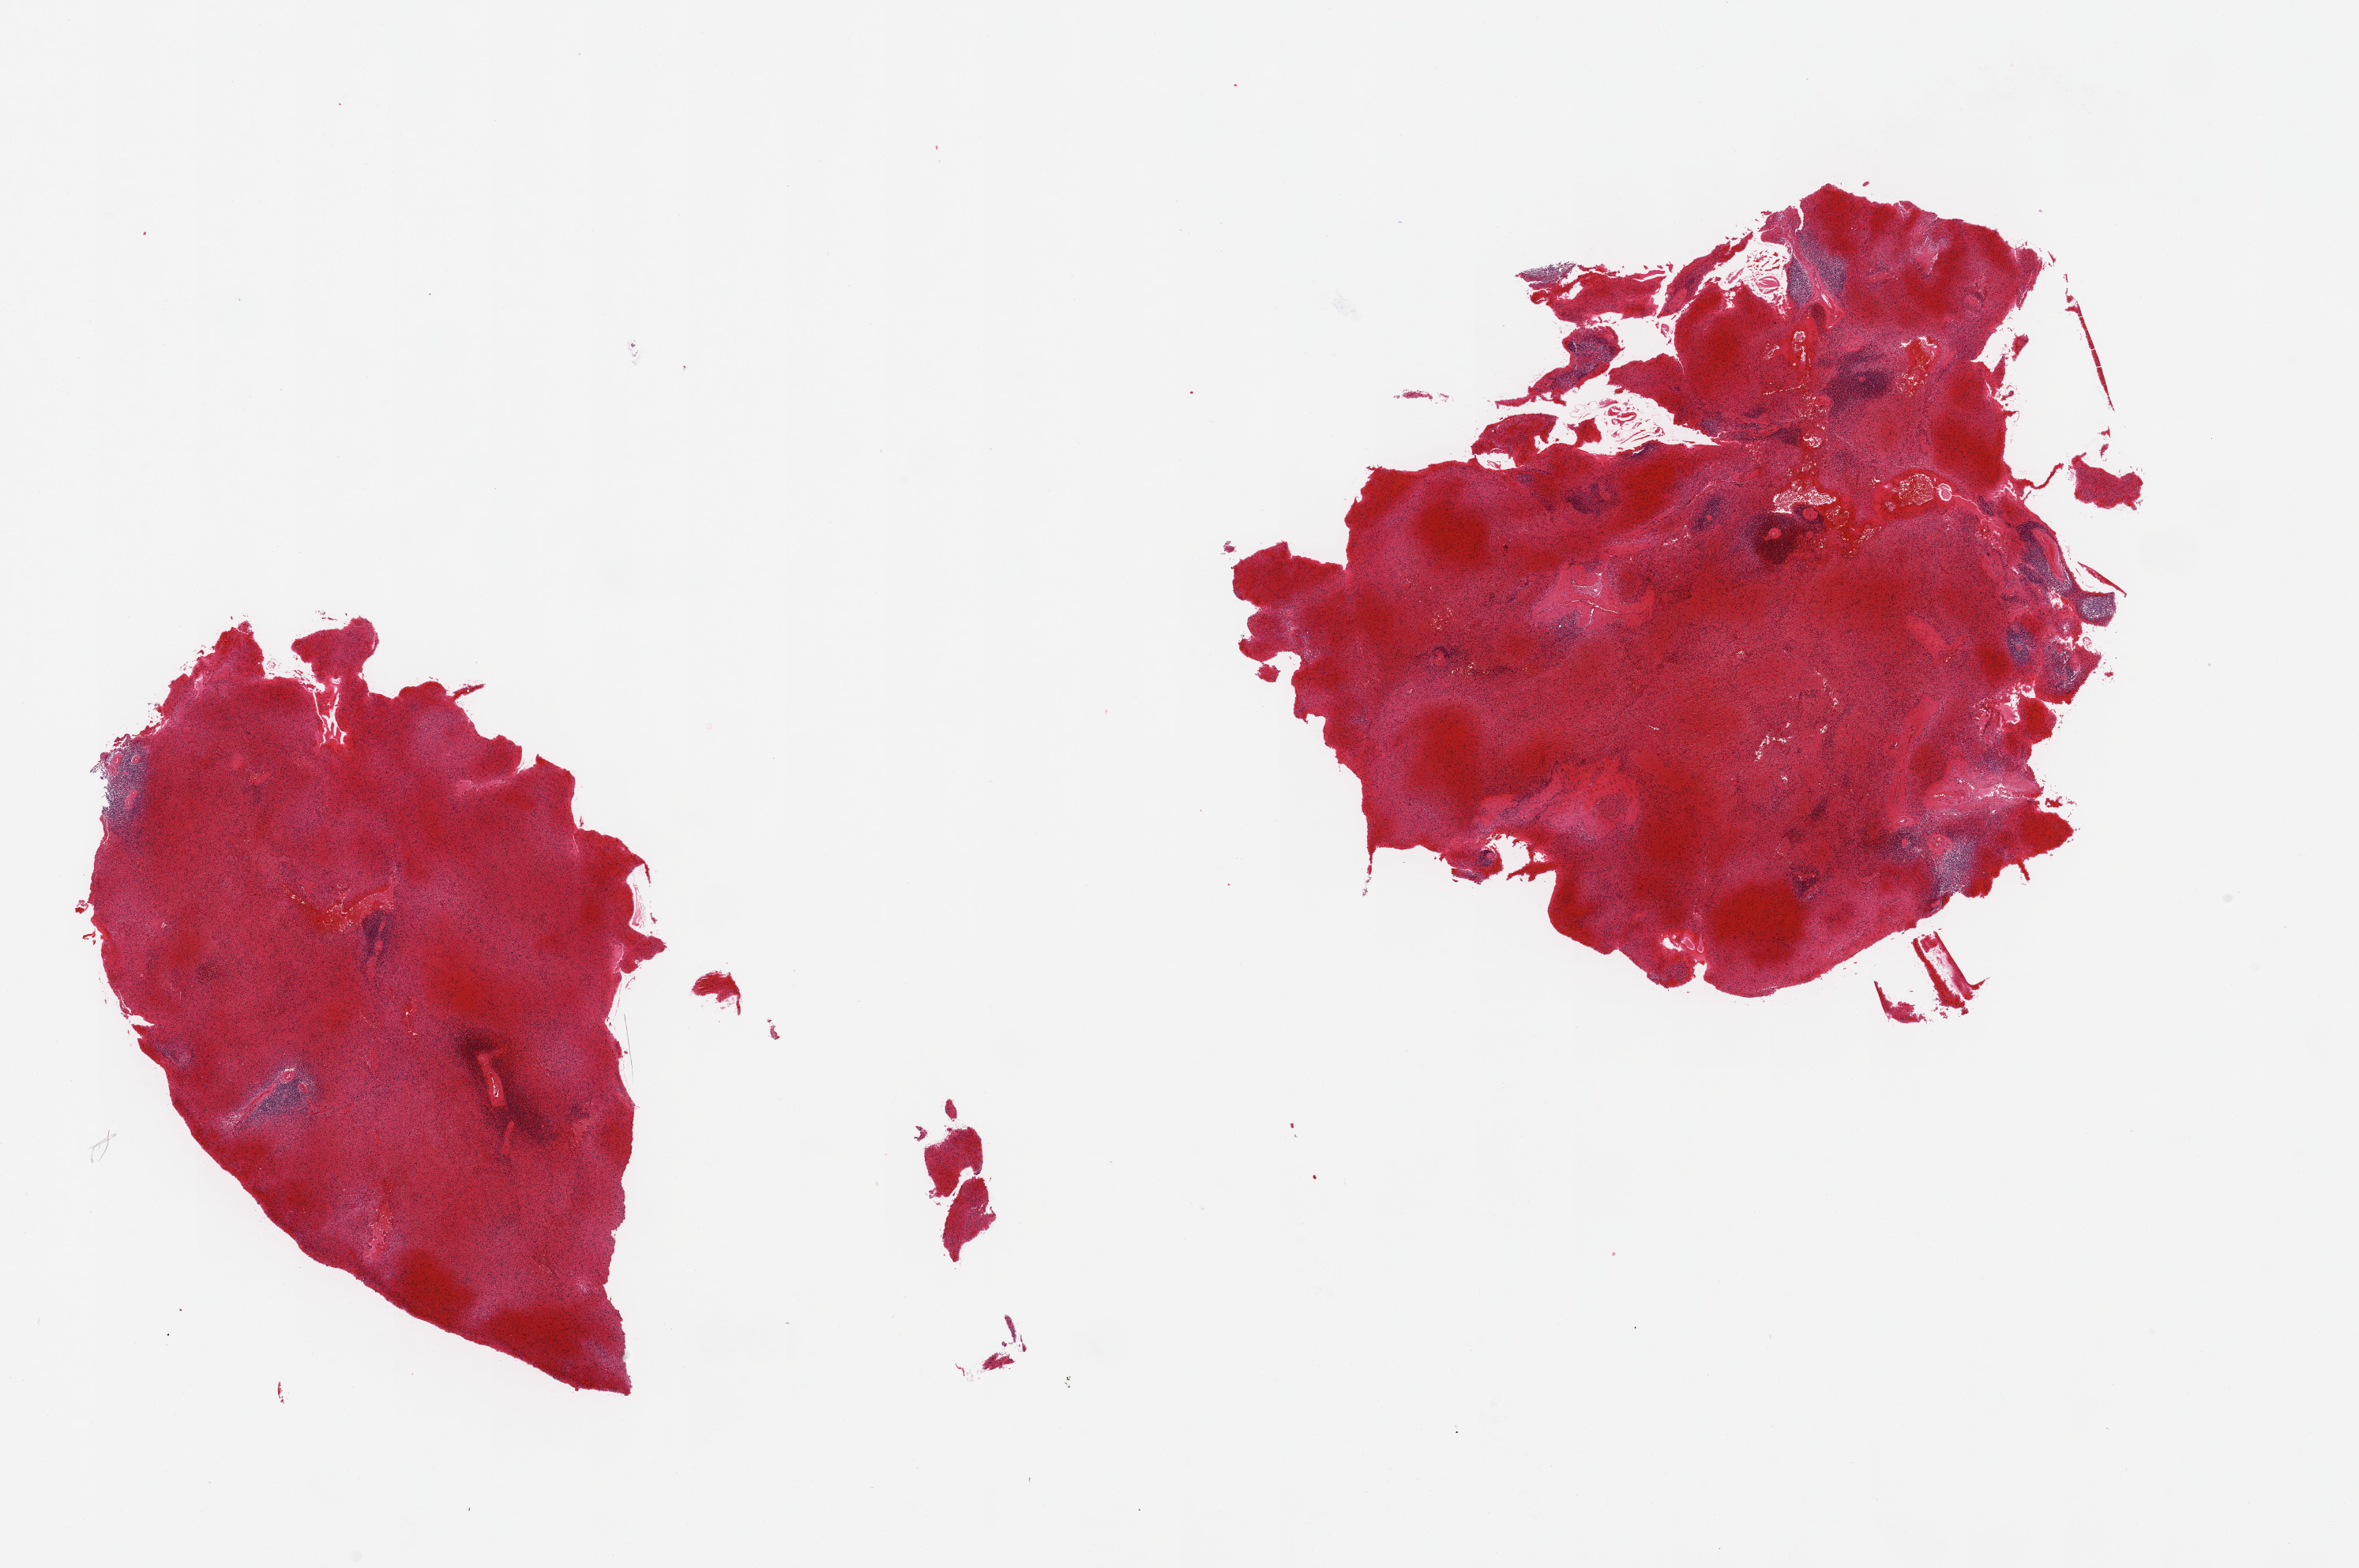
Hematoxylin and eosin (H&E) whole-slide image — shown as a low-resolution overview of the whole scanned area (about 23.6 x 15.7 mm, slide scanned at 20x), PAXgene-fixed paraffin-embedded (PFPE) section, target tissue: spleen, donor tissue sample. Male donor.
Review note (as recorded): 2 pieces, marked congestion.